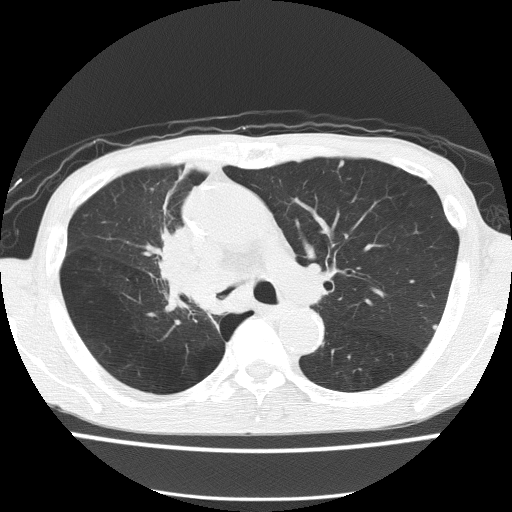
Low-dose screening chest CT, axial slice. Baseline screening round. Lung window (W 1500 / L -600 HU). Slice 54 of 150 in the series. Male participant, aged 59 years at enrolment. Former smoker at enrolment.
Expert reader's lesion annotation, bounding box [x1, y1, x2, y2] px = [140, 230, 233, 321]. The screening reader recorded 5 non-calcified nodules or masses ≥4 mm on this exam (left upper lobe, left upper lobe, left upper lobe, right middle lobe, right lower lobe); which of them this box marks is not recorded. Official screen result: positive, change unspecified: nodule(s) >= 4 mm or enlarging nodule(s), mass(es), or other non-specific abnormalities suspicious for lung cancer.